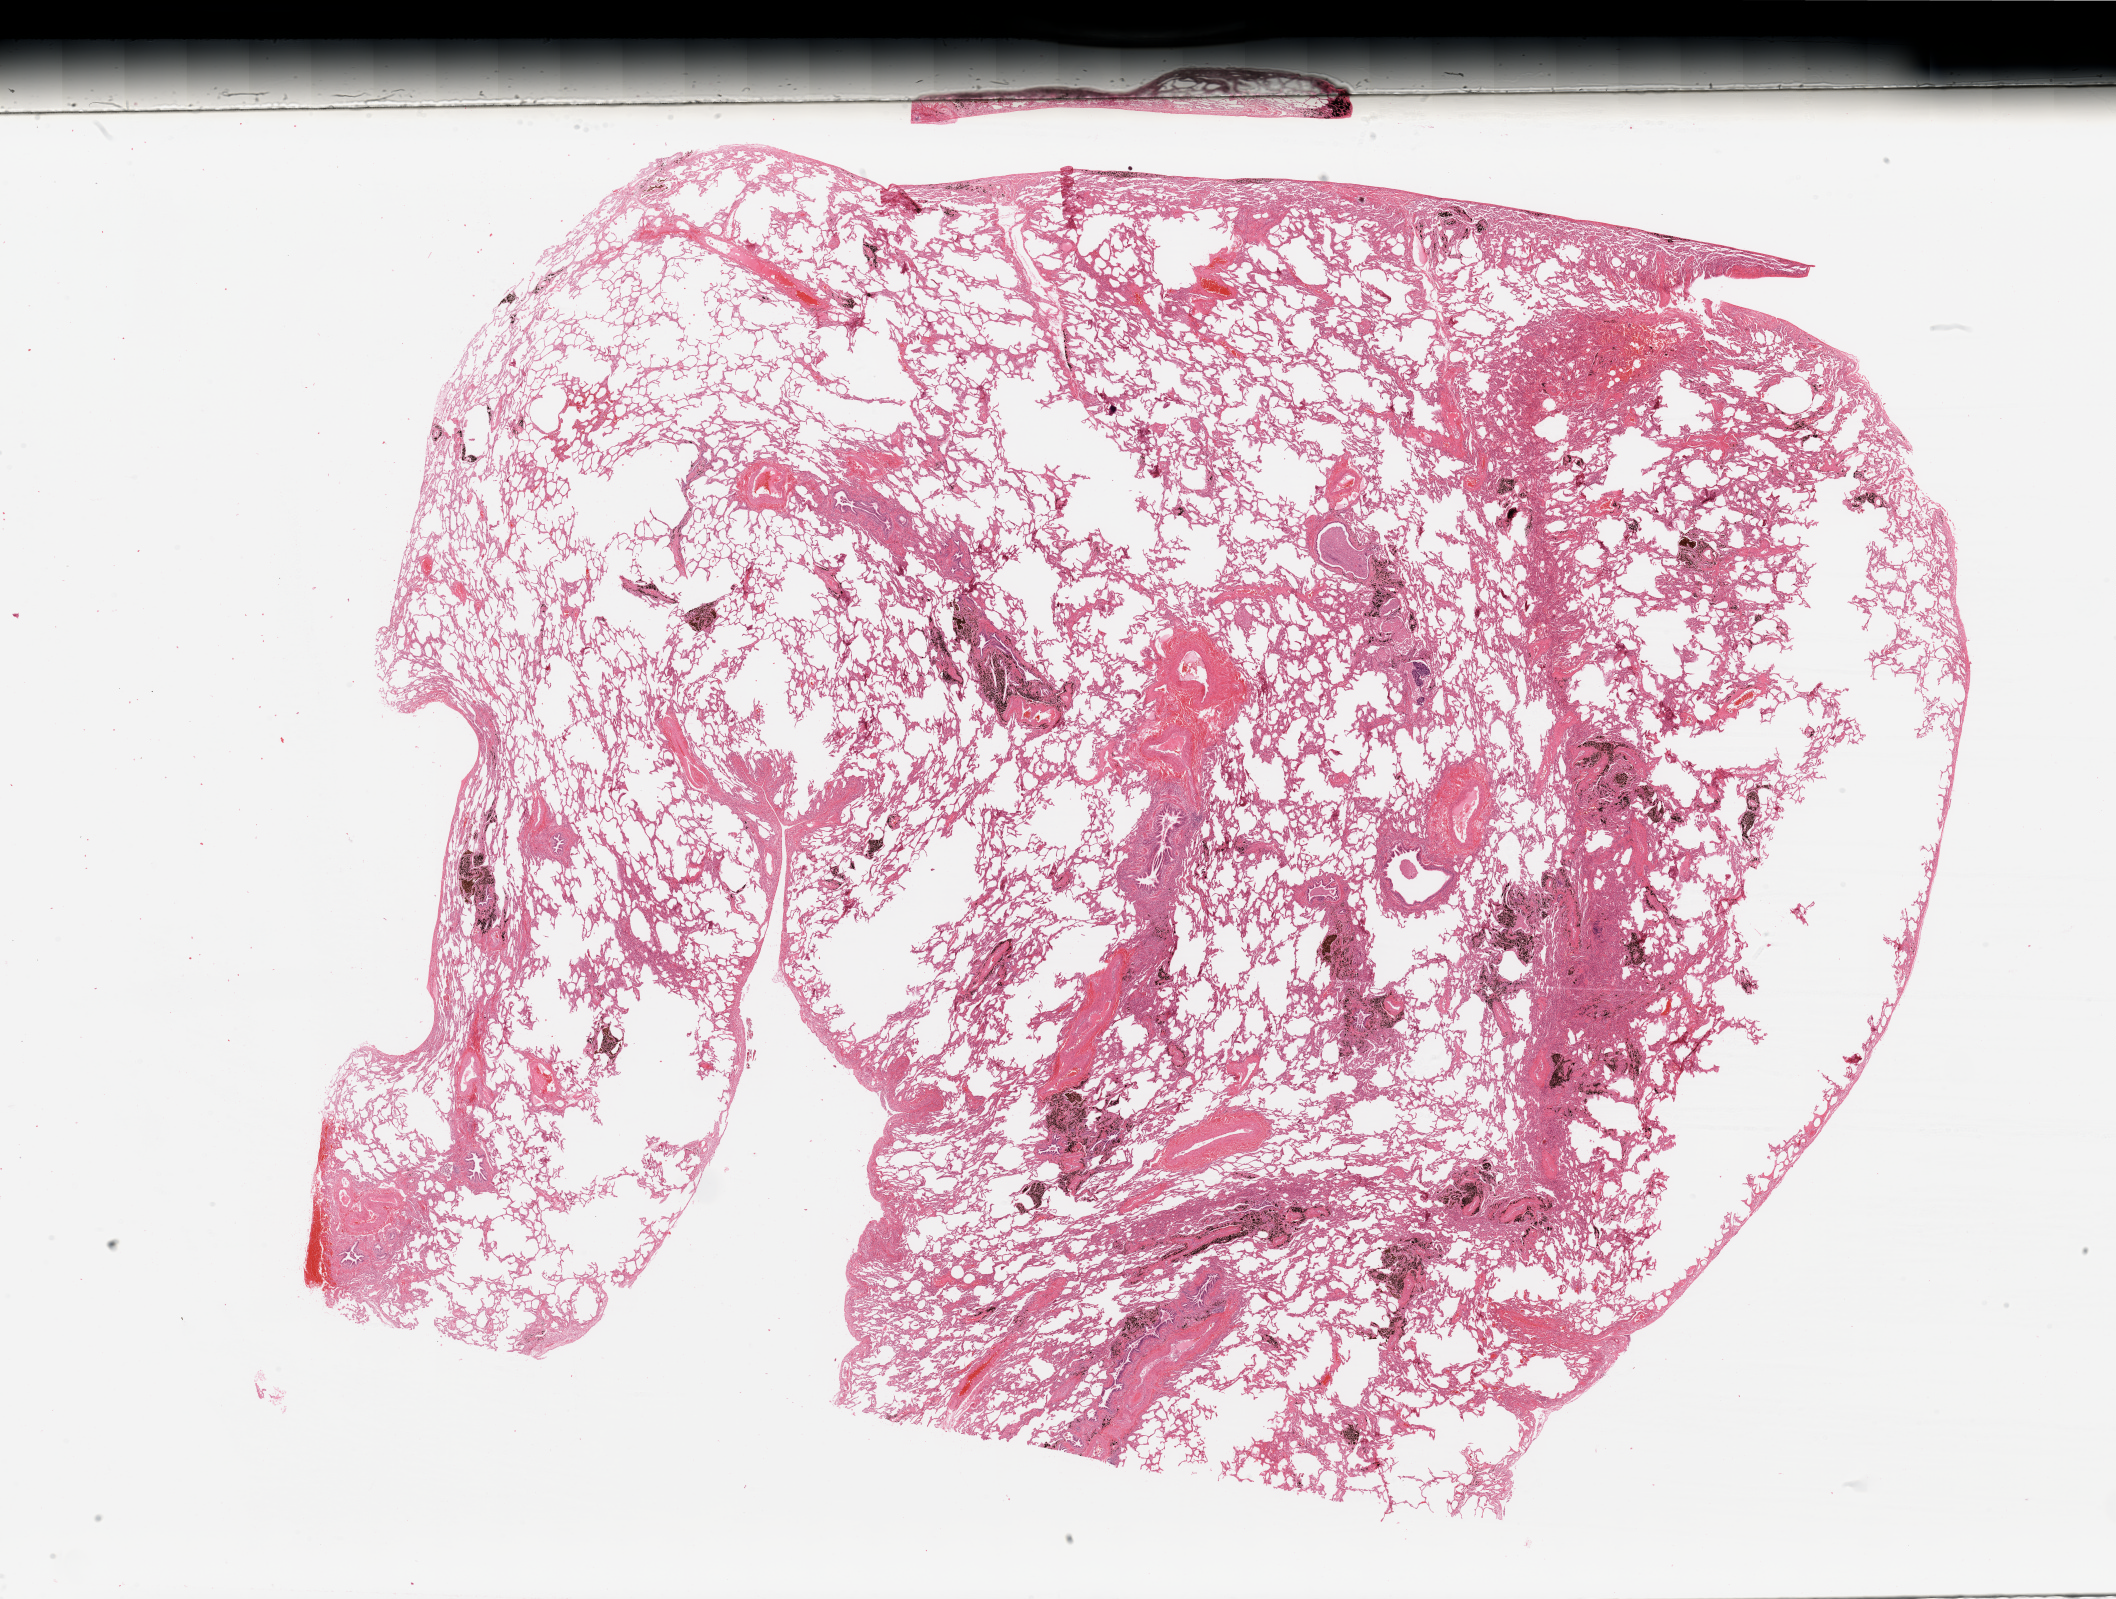
Whole-slide histology image, Hematoxylin and eosin (H&E) stained, a low-resolution overview of the entire scanned area, about 33.5 x 25.3 mm, normal (non-tumour) tissue sample, sampled site: lung. Male, 49 y/o.
This section: normal (non-tumour) tissue from the same patient. Patient diagnosis: Adenocarcinoma, NOS.